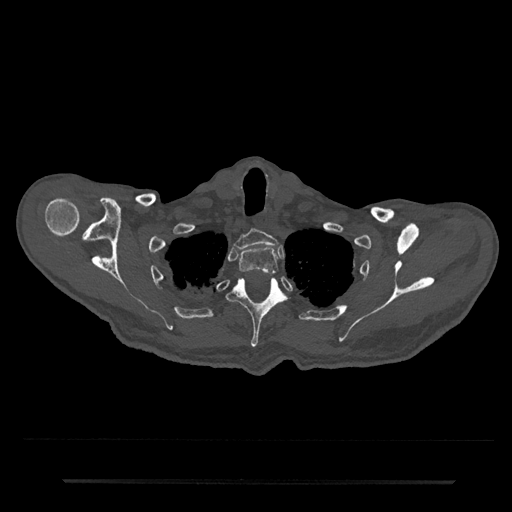
CT including the spine, one axial slice; position 673 of 797 along the scan axis; 120 kVp; bone window (W 1800 / L 400 HU); 0.5 mm slice thickness; 512 × 512 image matrix, field of view 427 × 427 mm. Male patient, age 74 years. Case-level facts recorded for this patient, not image findings: primary cancer: prostate.
Outlined on this slice (semi-automatically segmented with operator editing):
- T1 vertebra: bounding box (x1, y1, x2, y2) in pixels: (234, 229, 278, 250)
- T2 vertebra: (239, 247, 279, 276)
- T3 vertebra: (227, 275, 286, 347)